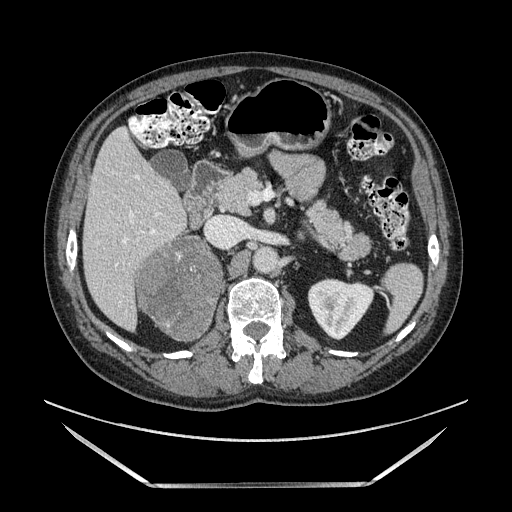
Contrast-enhanced abdominal CT, one axial slice; slice 72 of 185 in the series (ordered by position); soft-tissue window (W 400 / L 40 HU); 1.25 mm slice thickness; 512 × 512 image matrix, field of view 440 × 440 mm. Male patient. From the clinical record (not read from this slice): diagnosis: adrenocortical carcinoma; tumour side: right adrenal; tumour size at pathology: 10.3 cm; Ki-67 index: 20 %; stage (as recorded): 3.
Structures marked on this image (semi-automatically segmented with operator editing):
- mass: bounding box [x1, y1, x2, y2] px = [138, 240, 222, 339]